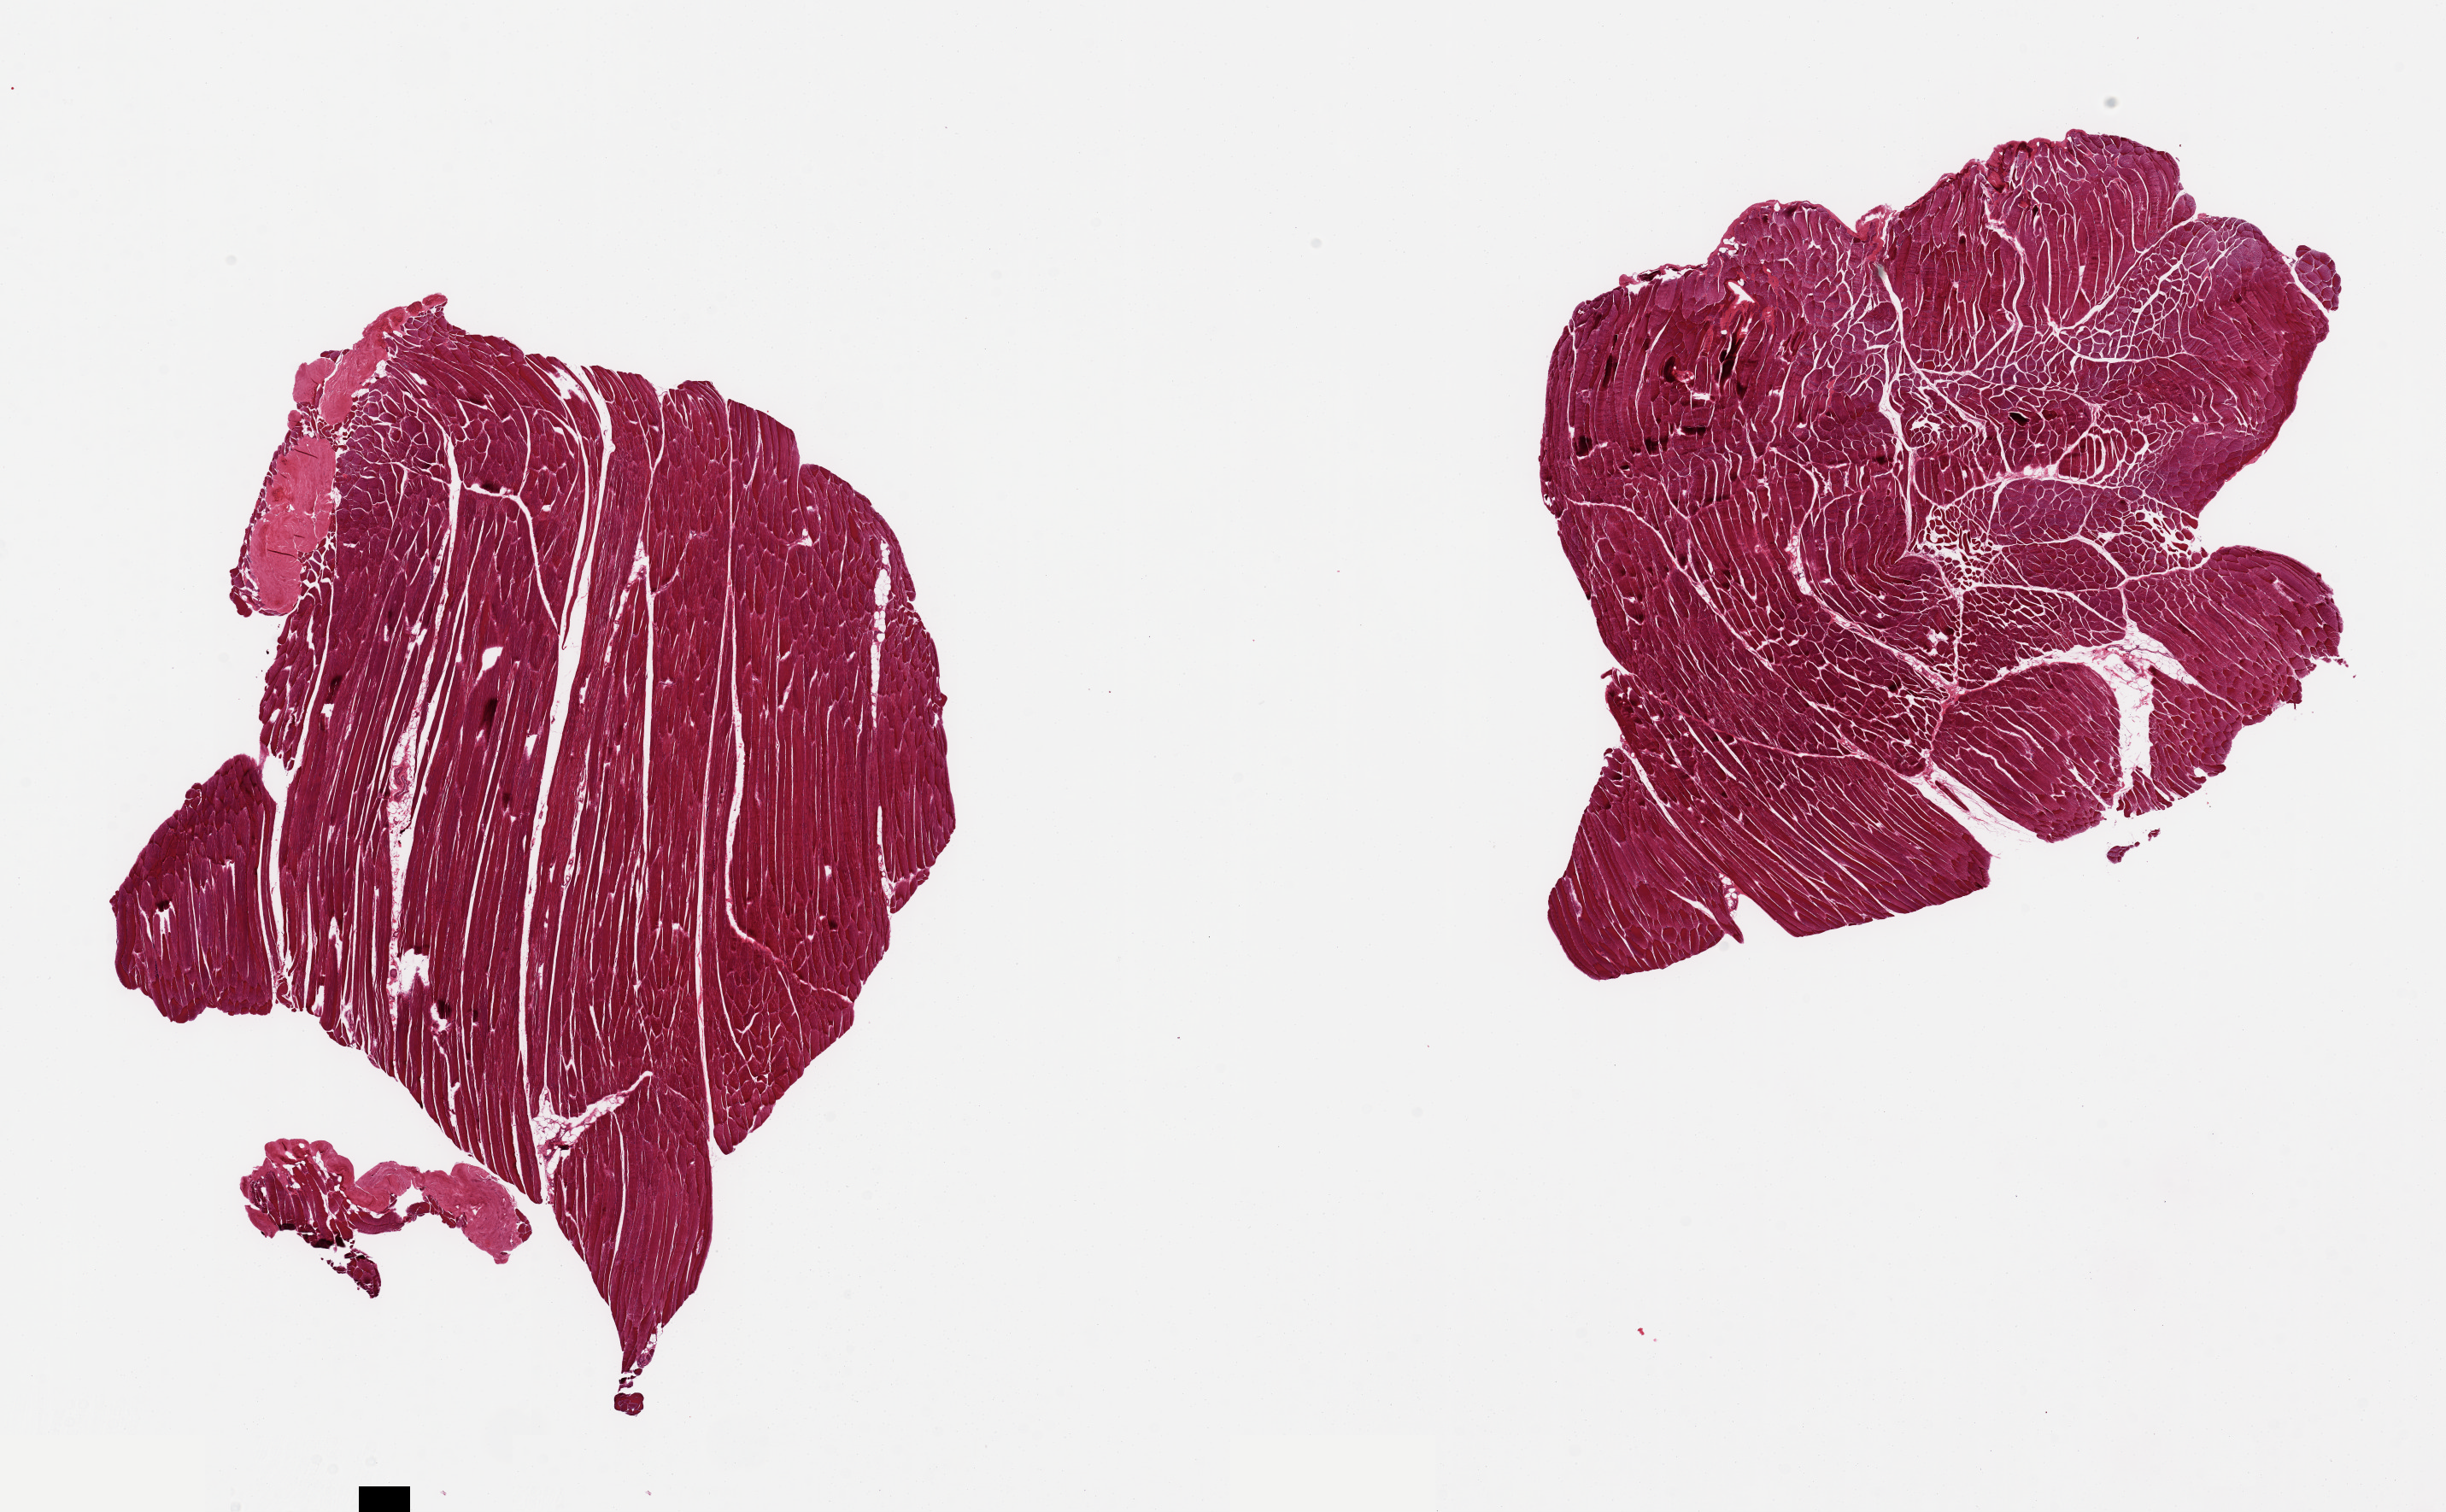
Digitized H&E-stained section, a low-resolution overview of the entire scanned area, about 22.6 x 14.0 mm (acquisition: 20x scan); PAXgene-fixed, paraffin-embedded tissue; sampled site (target tissue): skeletal muscle; tissue donor sample.
Pathologist's review note for this sample: 2 pieces.